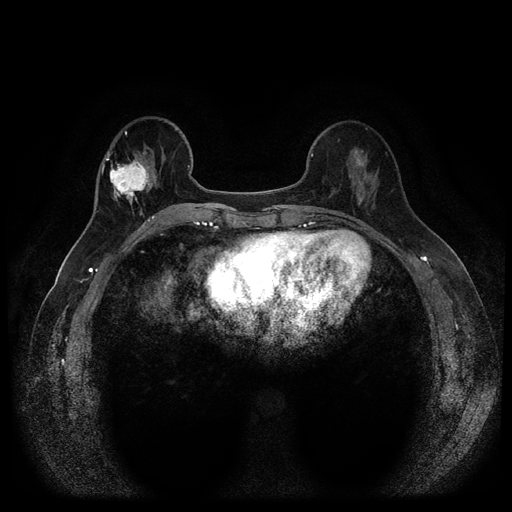
Breast MRI (dynamic contrast-enhanced, multi-phase), one axial slice; position 36 of 116 along the scan axis; dynamic contrast-enhanced series, time point 2 of 5 at this slice position (early post-contrast); 1.5 T; TE 2.6 ms, TR 5.4 ms; 2 mm slice thickness; 512 × 512 image matrix, field of view 340 × 340 mm. Patient: female, 56 years.
Structures marked on this image (semi-automatically segmented with operator editing):
- breast lesion (labelled benign in the annotation): bounding box [x1, y1, x2, y2] px = [348, 149, 372, 208]
- breast lesion (labelled 'tumour' in the annotation; benign lesions carry a separate 'benign' label): [108, 152, 156, 208]